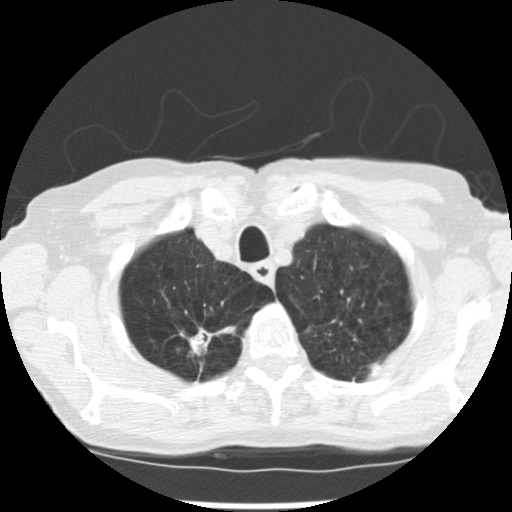
Low-dose screening chest CT, axial slice; first (baseline) screen; lung window (W 1500 / L -600 HU); 2.5 mm slice thickness; slice 31 of 265 in the series. Female participant, aged 72 years at enrolment.
- Expert-annotated lung lesion, bounding box (x1, y1, x2, y2) in pixels: (176, 314, 232, 356).
- The screening reader recorded 3 non-calcified nodules or masses ≥4 mm on this exam (right upper lobe, left upper lobe, left lower lobe); which of them this box marks is not recorded.
- Official screen result: positive, change unspecified: nodule(s) >= 4 mm or enlarging nodule(s), mass(es), or other non-specific abnormalities suspicious for lung cancer.
- Lung cancer was diagnosed 50 days after this screen: adenocarcinoma, NOS, right upper lobe, moderately differentiated (G2), stage IB (AJCC 6th edition), 22 mm at pathology.